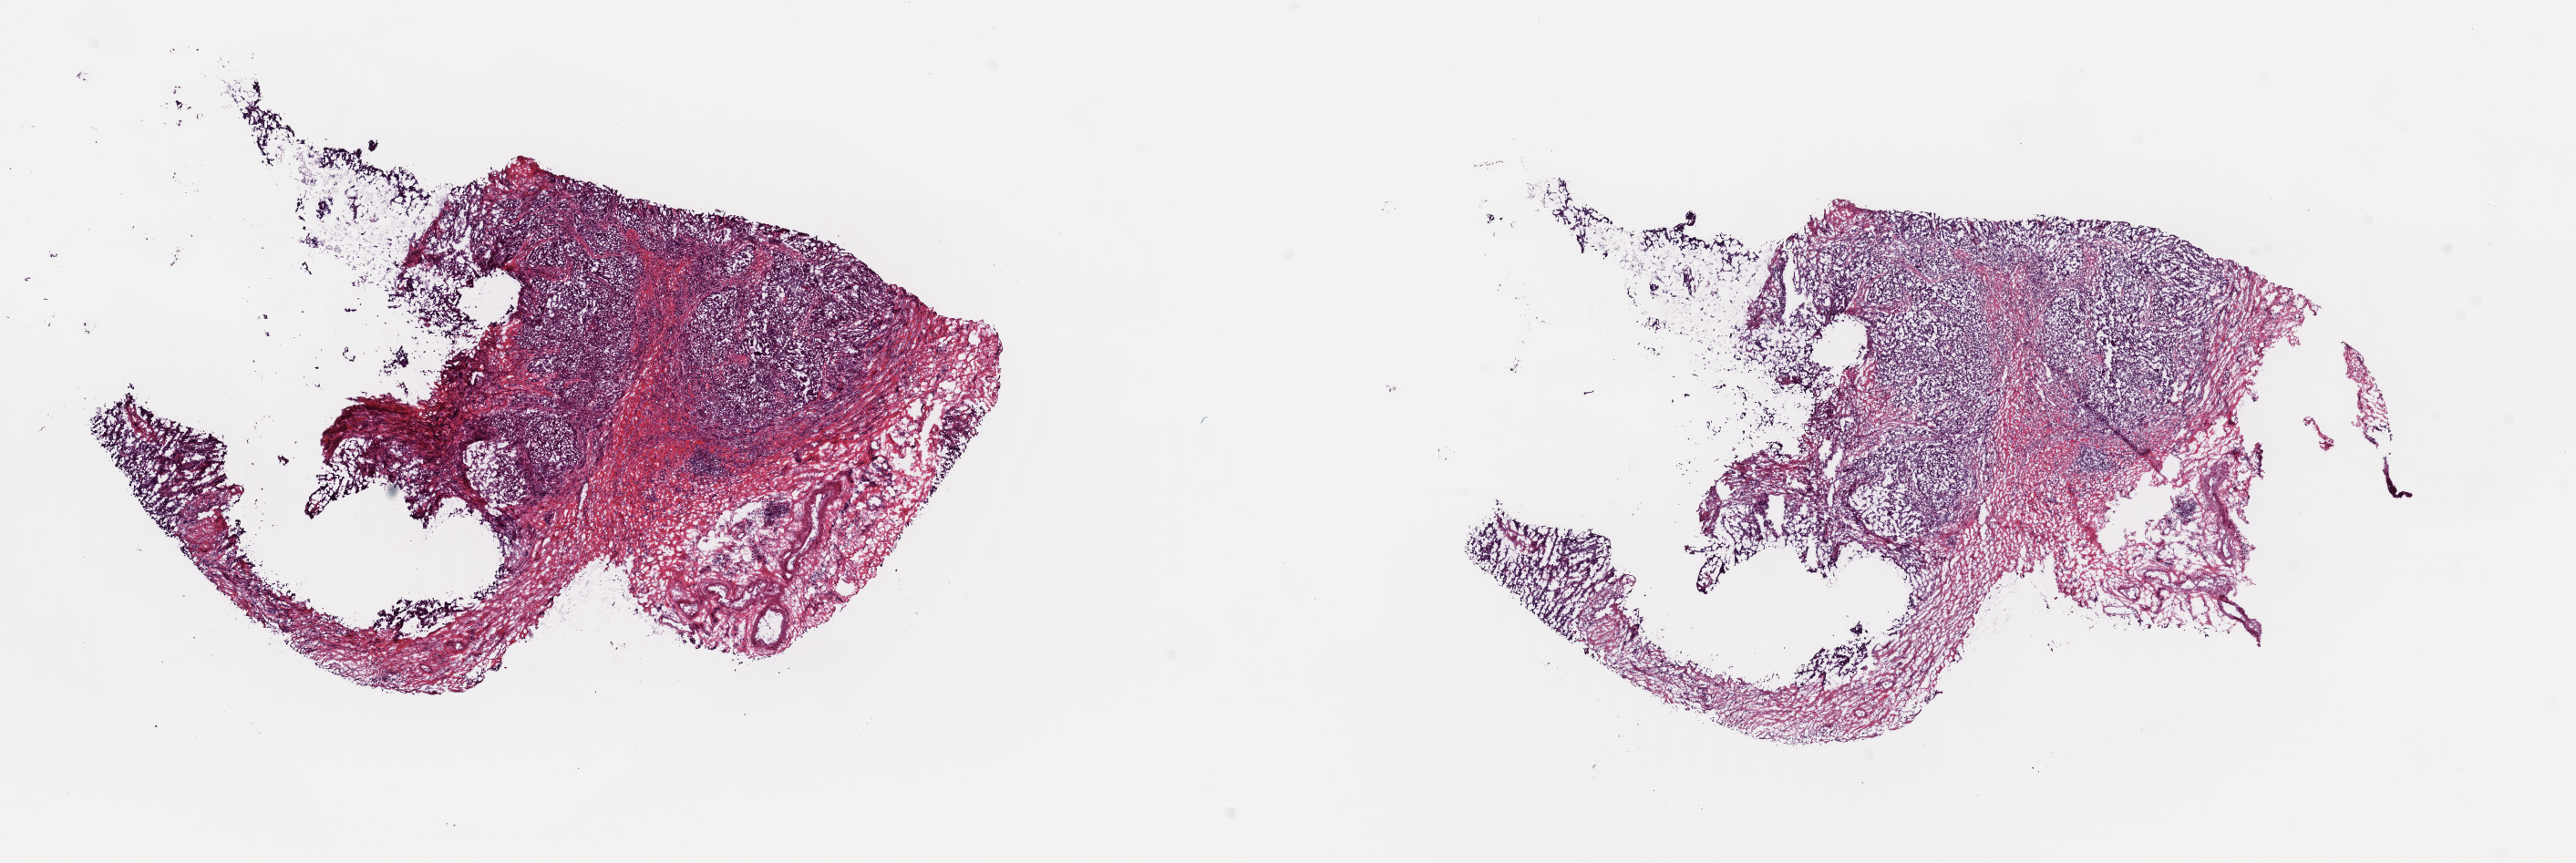
Digitized H&E tissue section (whole slide) — shown as a low-resolution overview of the whole scanned area (about 22.3 x 7.5 mm, from a 40x scan), frozen section from the top of the tissue portion, thyroid, primary tumour sample. Female patient; age at initial diagnosis 83 years. Pathologist review of this section (percent, as recorded): tumour cells 50%, tumour nuclei 100%, normal cells 0%, stromal cells 50%, necrosis 0%. Infiltration values recorded for this section: lymphocyte infiltration 2%, monocyte infiltration 2%, neutrophil infiltration 0%.
• AJCC pathologic stage: III (7th edition)
• pathologic diagnosis: Papillary adenocarcinoma, NOS
• TNM: T2 N1a MX
• laterality: right